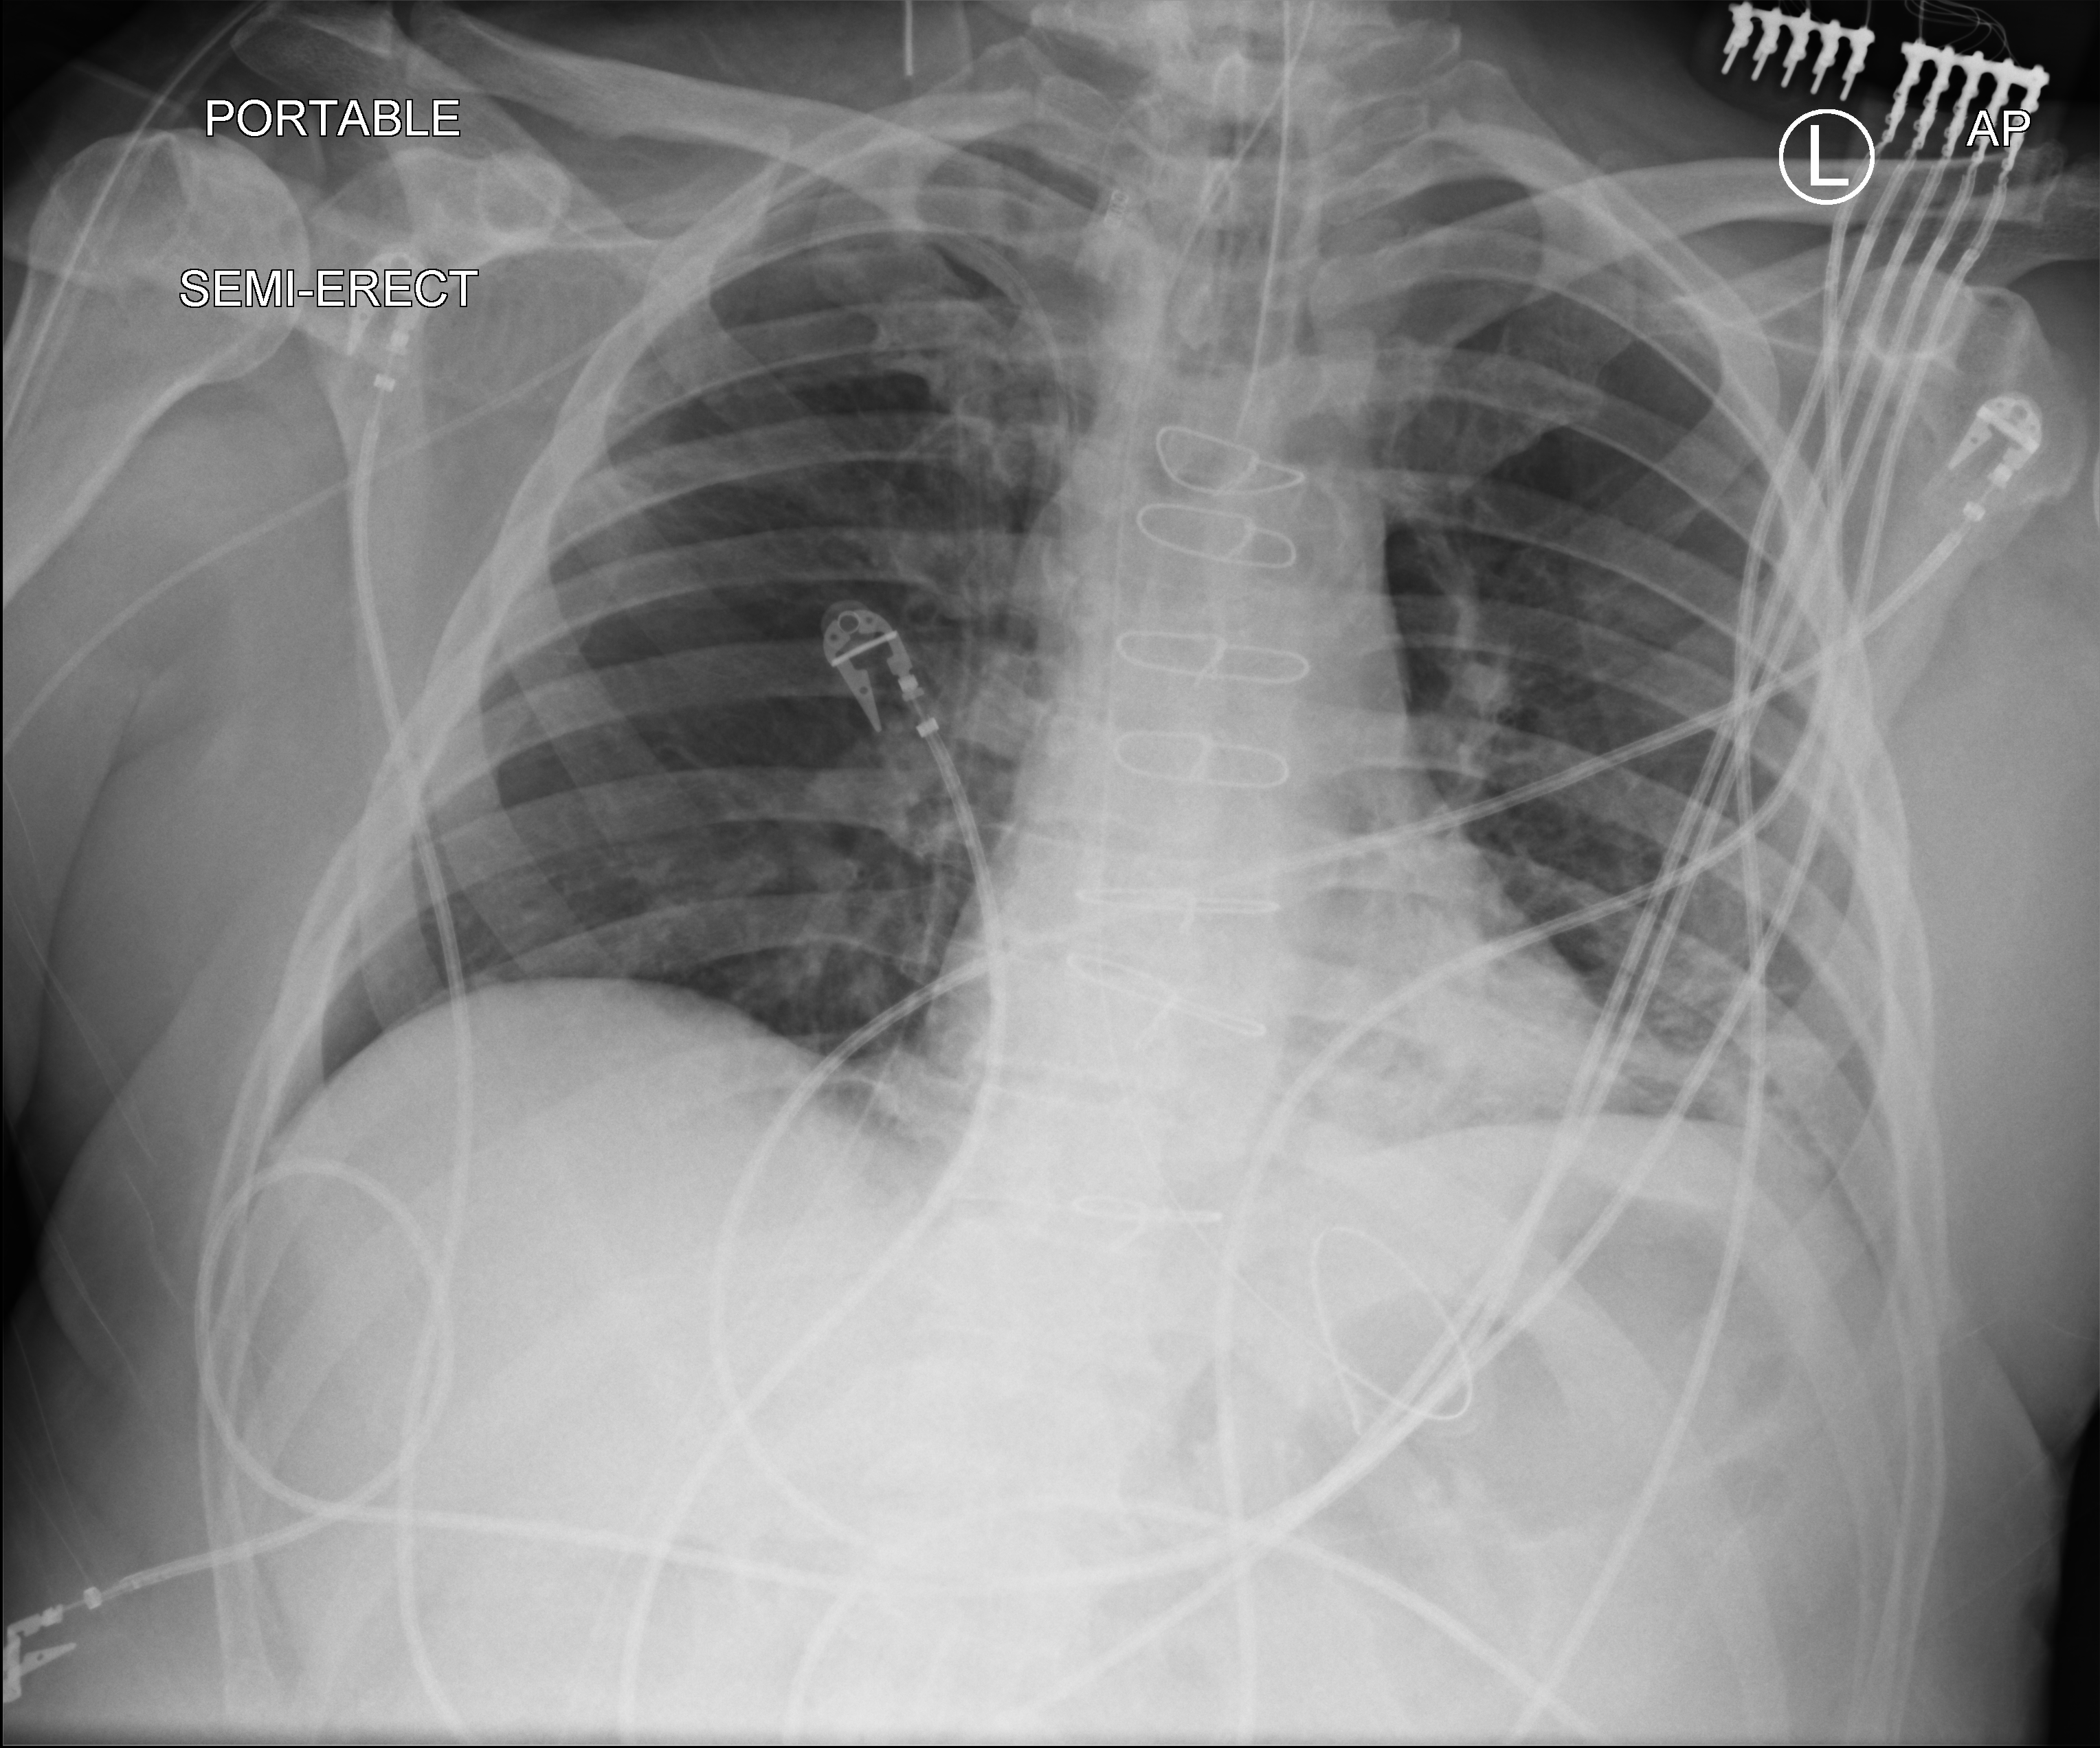
Bedside chest radiograph (computed radiography); anteroposterior (AP) projection. Male patient hospitalised with COVID-19, age 60–74 years.
From the hospital-stay record, not from the radiograph (when in the stay this image was taken is not recorded): hypertension (admission record): yes; admitted to intensive care during this hospital stay: yes; mechanically ventilated during this hospital stay: yes.